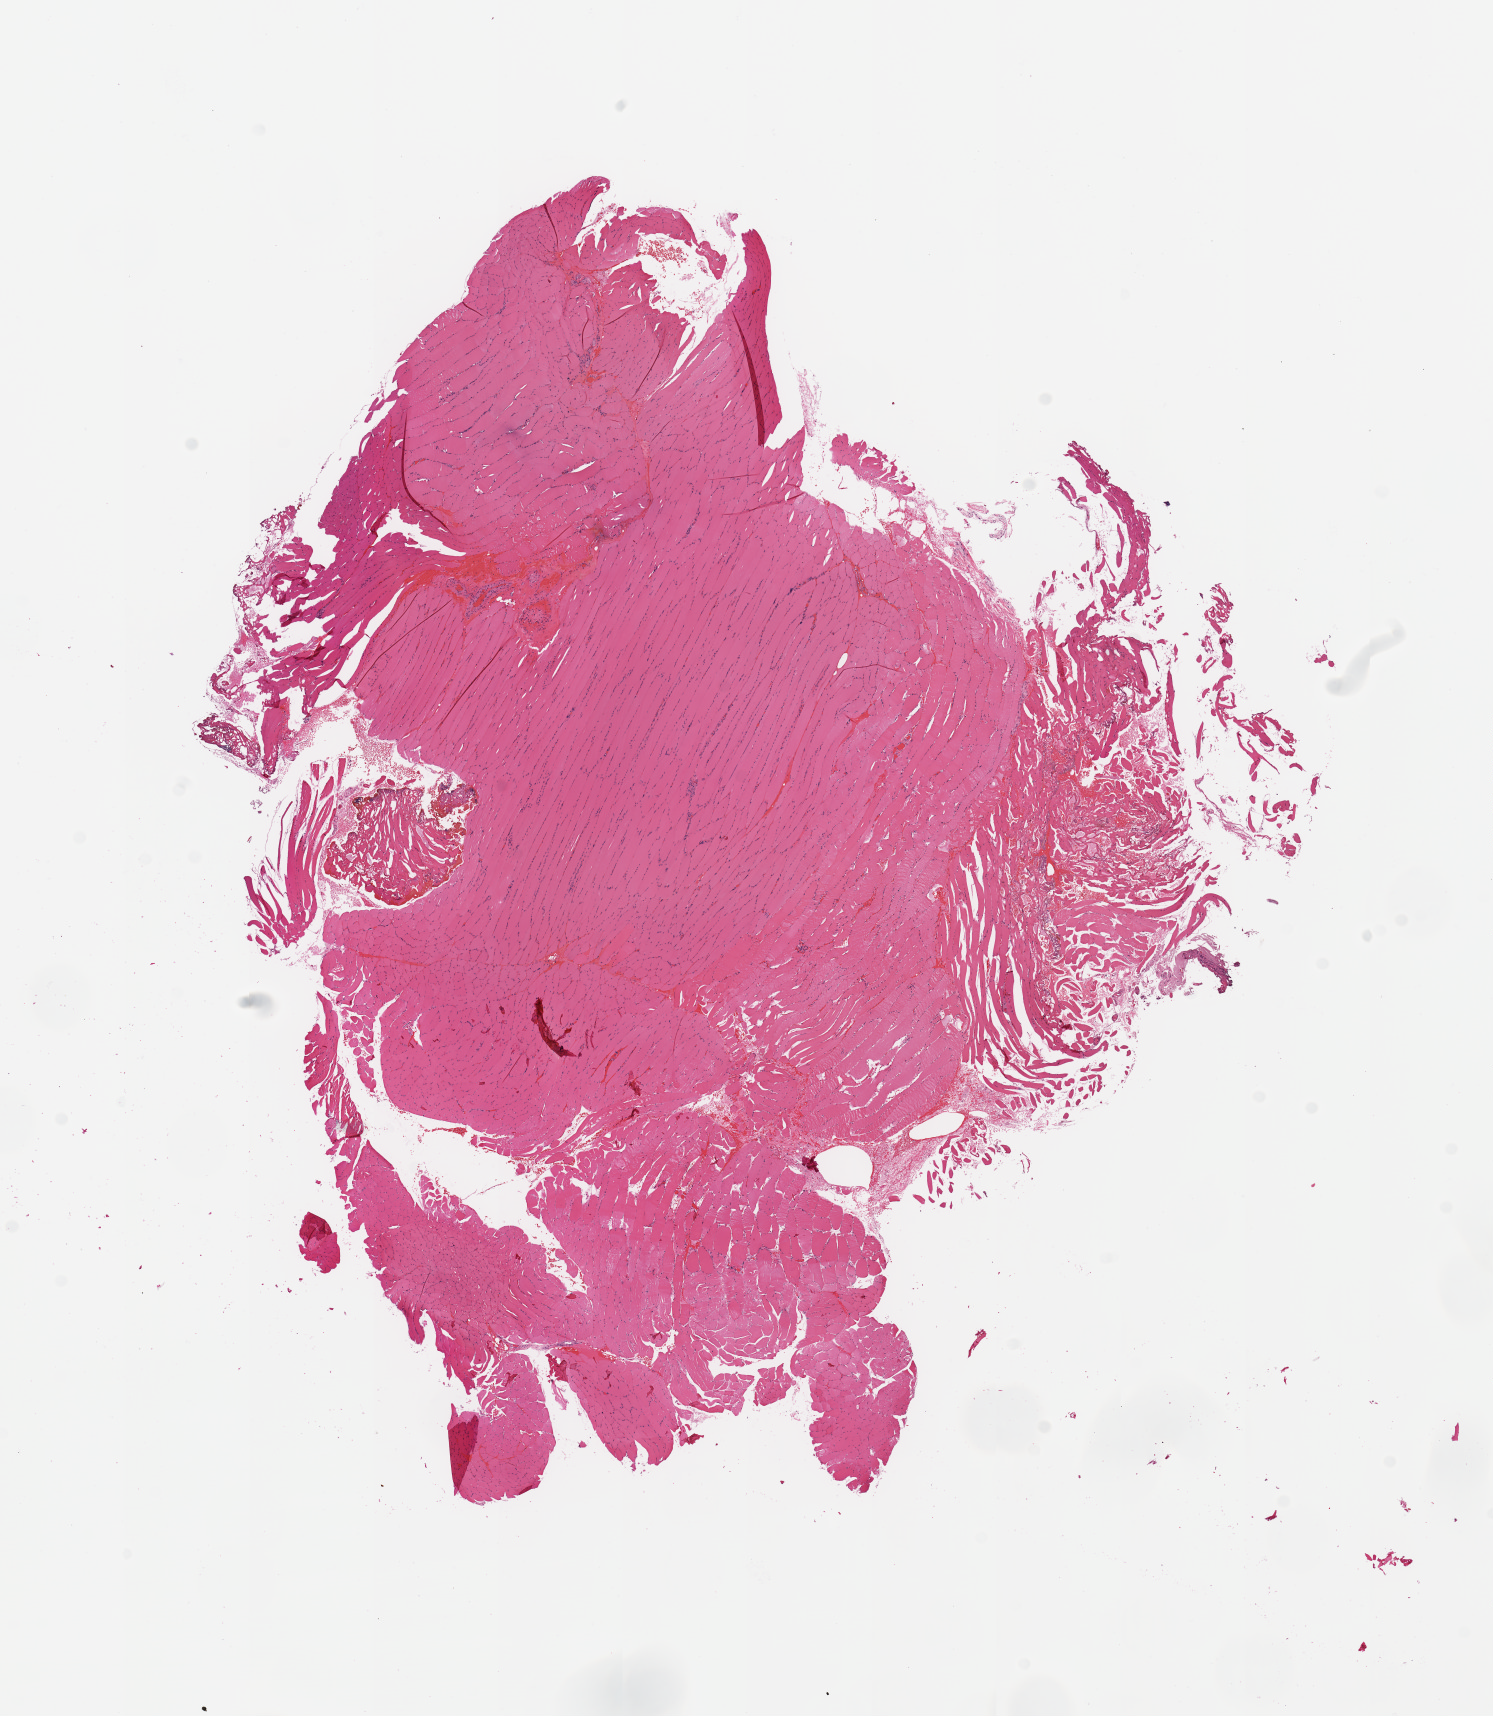
H&E whole-slide image, a low-resolution overview of the entire scanned area, about 11.8 x 13.6 mm (acquisition: 20x scan). Normal (non-tumour) tissue sample. Patient: male, age 78 years.
This section: normal (non-tumour) tissue from the same patient. Patient diagnosis (cohort enrolment): sarcoma (site not recorded at cohort level).